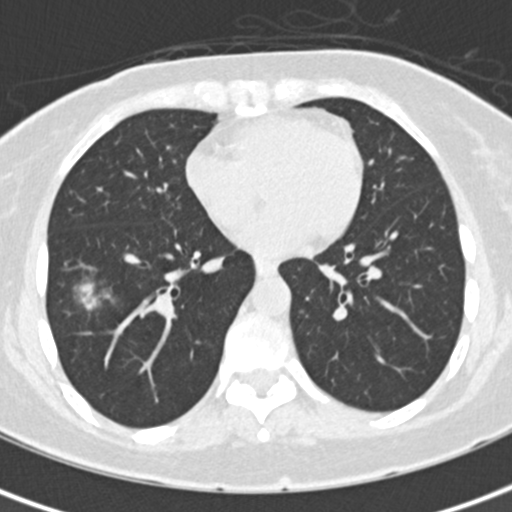
Axial slice from a low-dose chest CT screening exam; baseline annual screen; lung window (W 1500 / L -600 HU); 2 mm slice thickness. Female participant, aged 56 years at enrolment. Former smoker at enrolment.
Expert-annotated lung lesion, box from (x=62, y=270) to (x=127, y=327) px. The screening reader recorded 5 non-calcified nodules or masses ≥4 mm on this exam; which of them this box marks is not recorded.